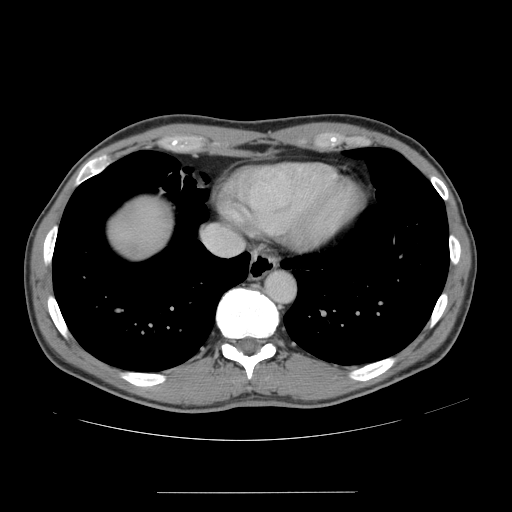
Contrast-enhanced abdominal CT, one axial slice; soft-tissue window (W 400 / L 40 HU); 512 × 512 image matrix, field of view 401 × 401 mm. Male patient, age 53 years. Case-level facts recorded for this patient, not image findings: diagnosis: colorectal cancer liver metastases, imaged before liver resection; multiple liver metastases: yes; largest metastasis: 2.4 cm; disease in both lobes: no.
Annotated regions visible in this slice (expert manual segmentation):
- liver: box from (x=110, y=198) to (x=168, y=258) px